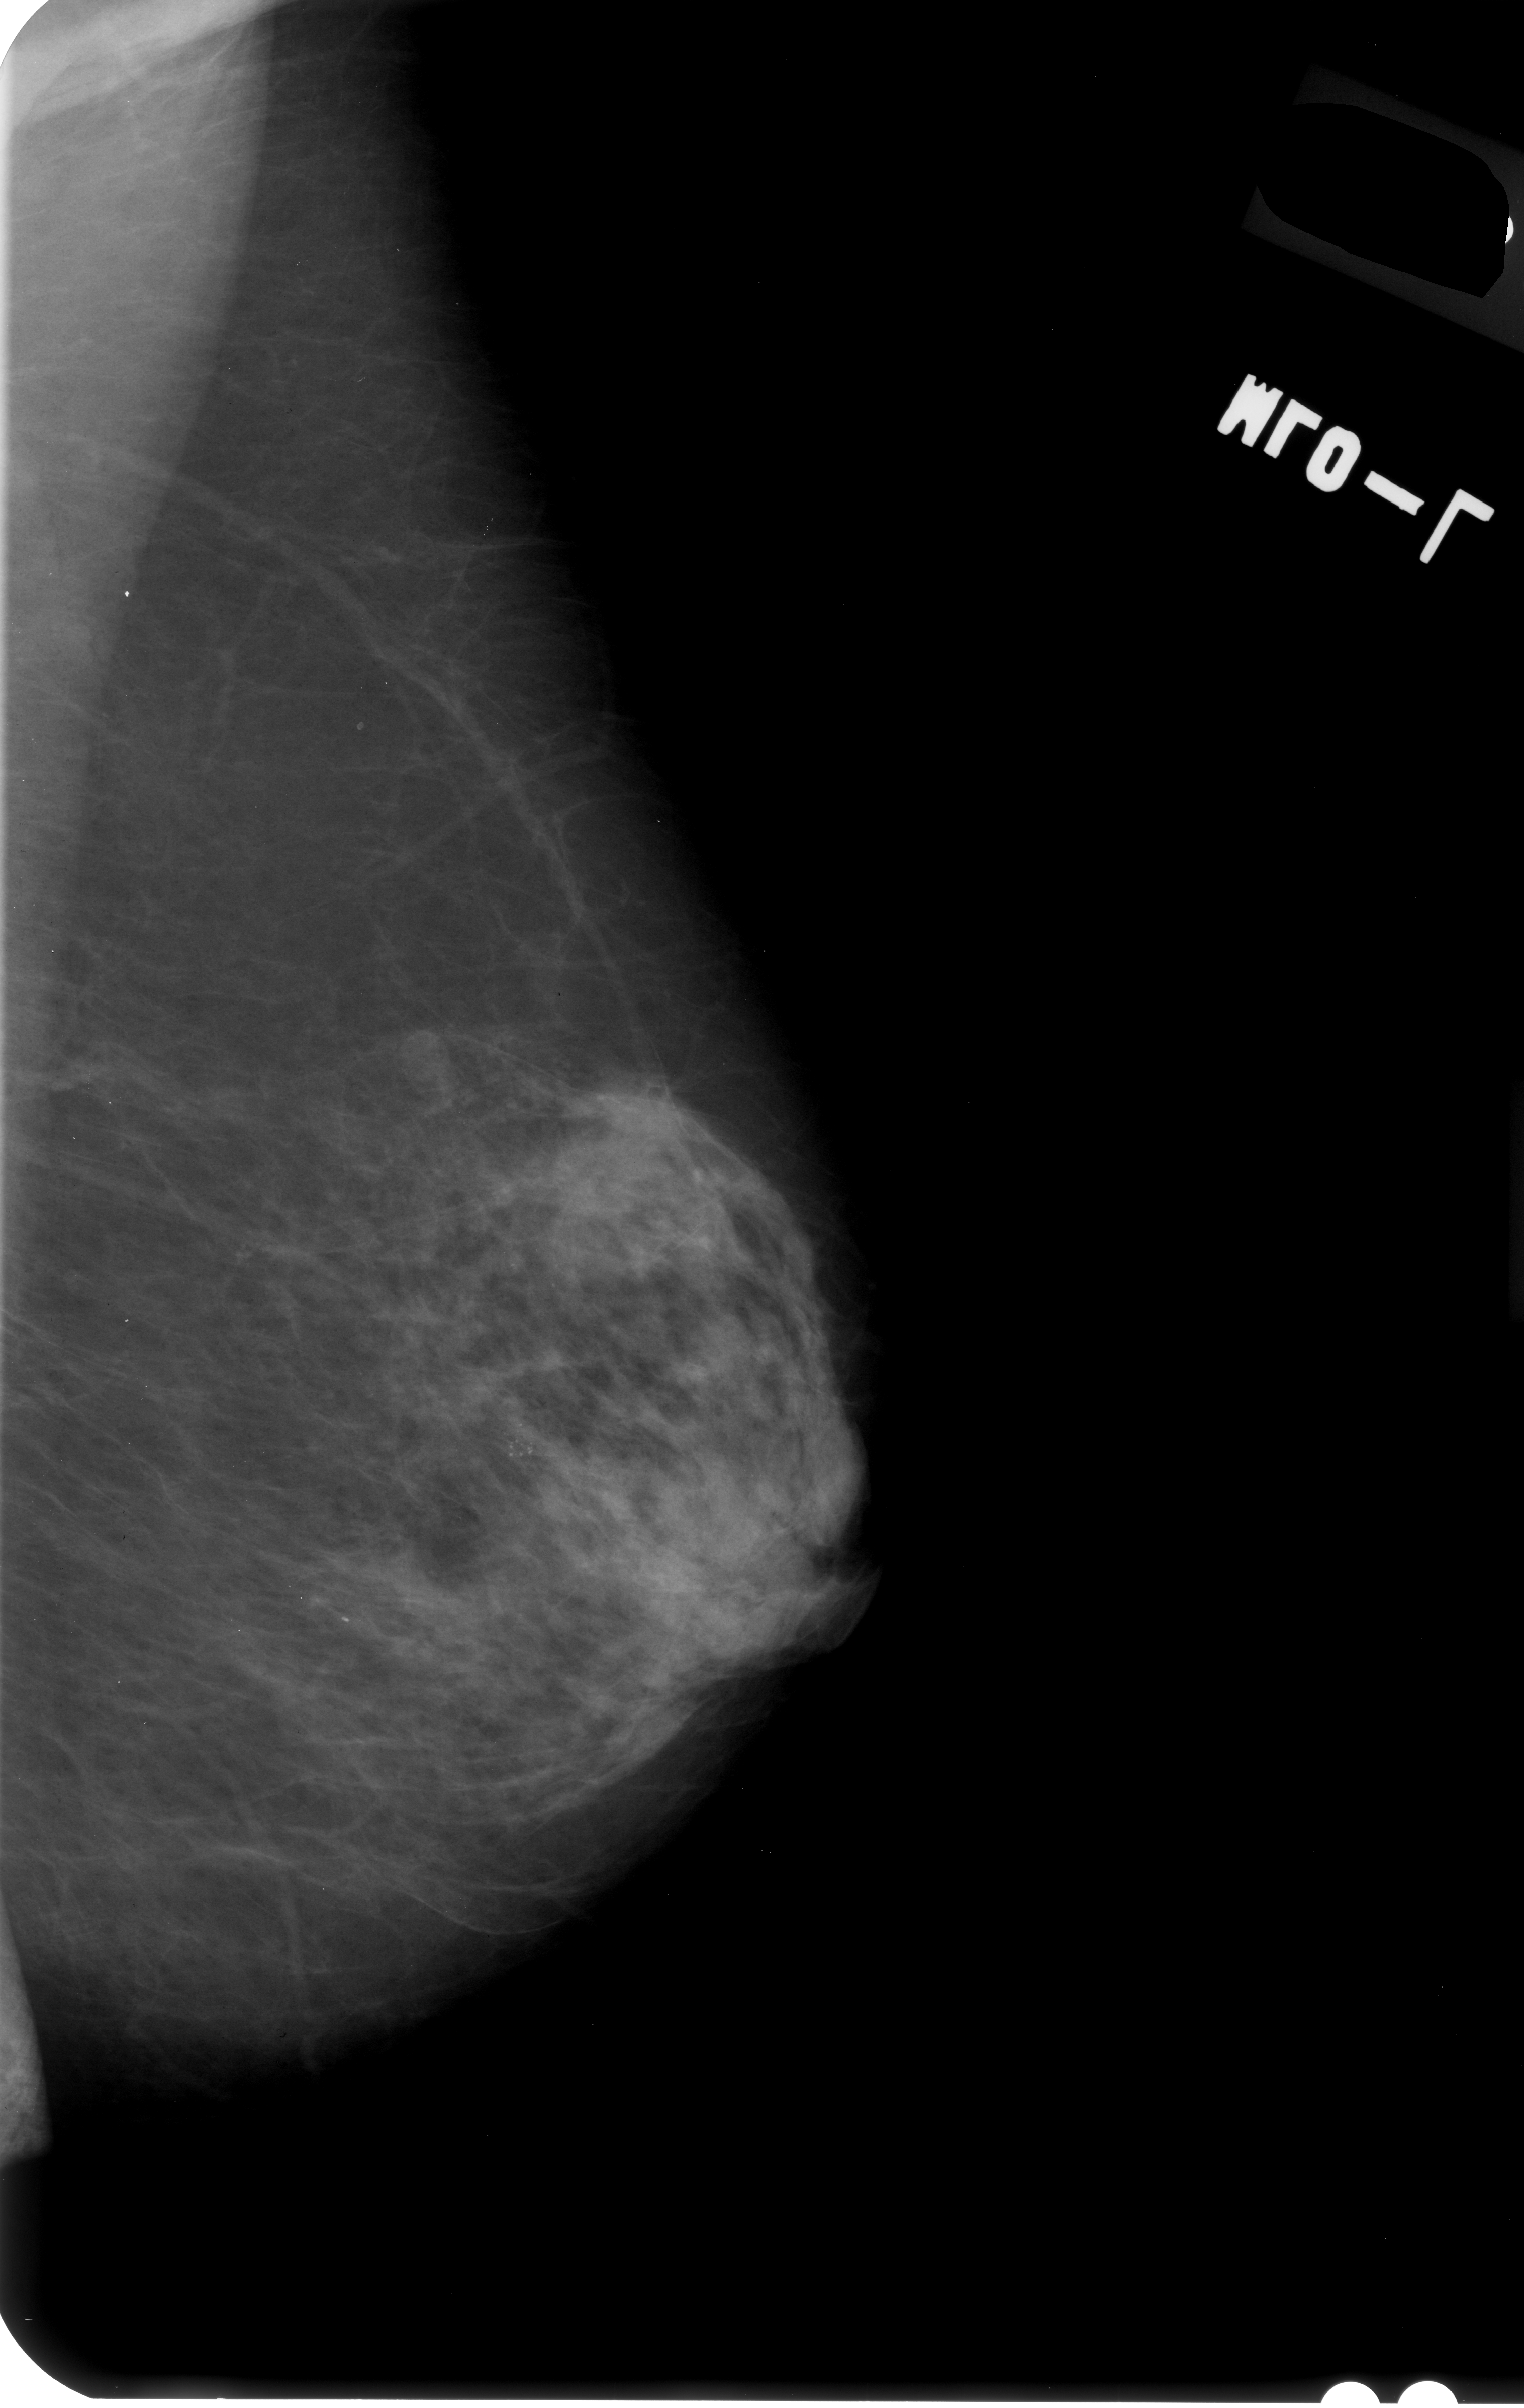
Digitized screen-film mammogram; left breast; MLO view.
Radiologist-marked abnormalities on this image: calcifications, morphology punctate / pleomorphic, distribution clustered; BI-RADS assessment category 4; subtlety rating 3 on a 1 (subtle) to 5 (obvious) scale; pathology result (as recorded, not read from the image): malignant.